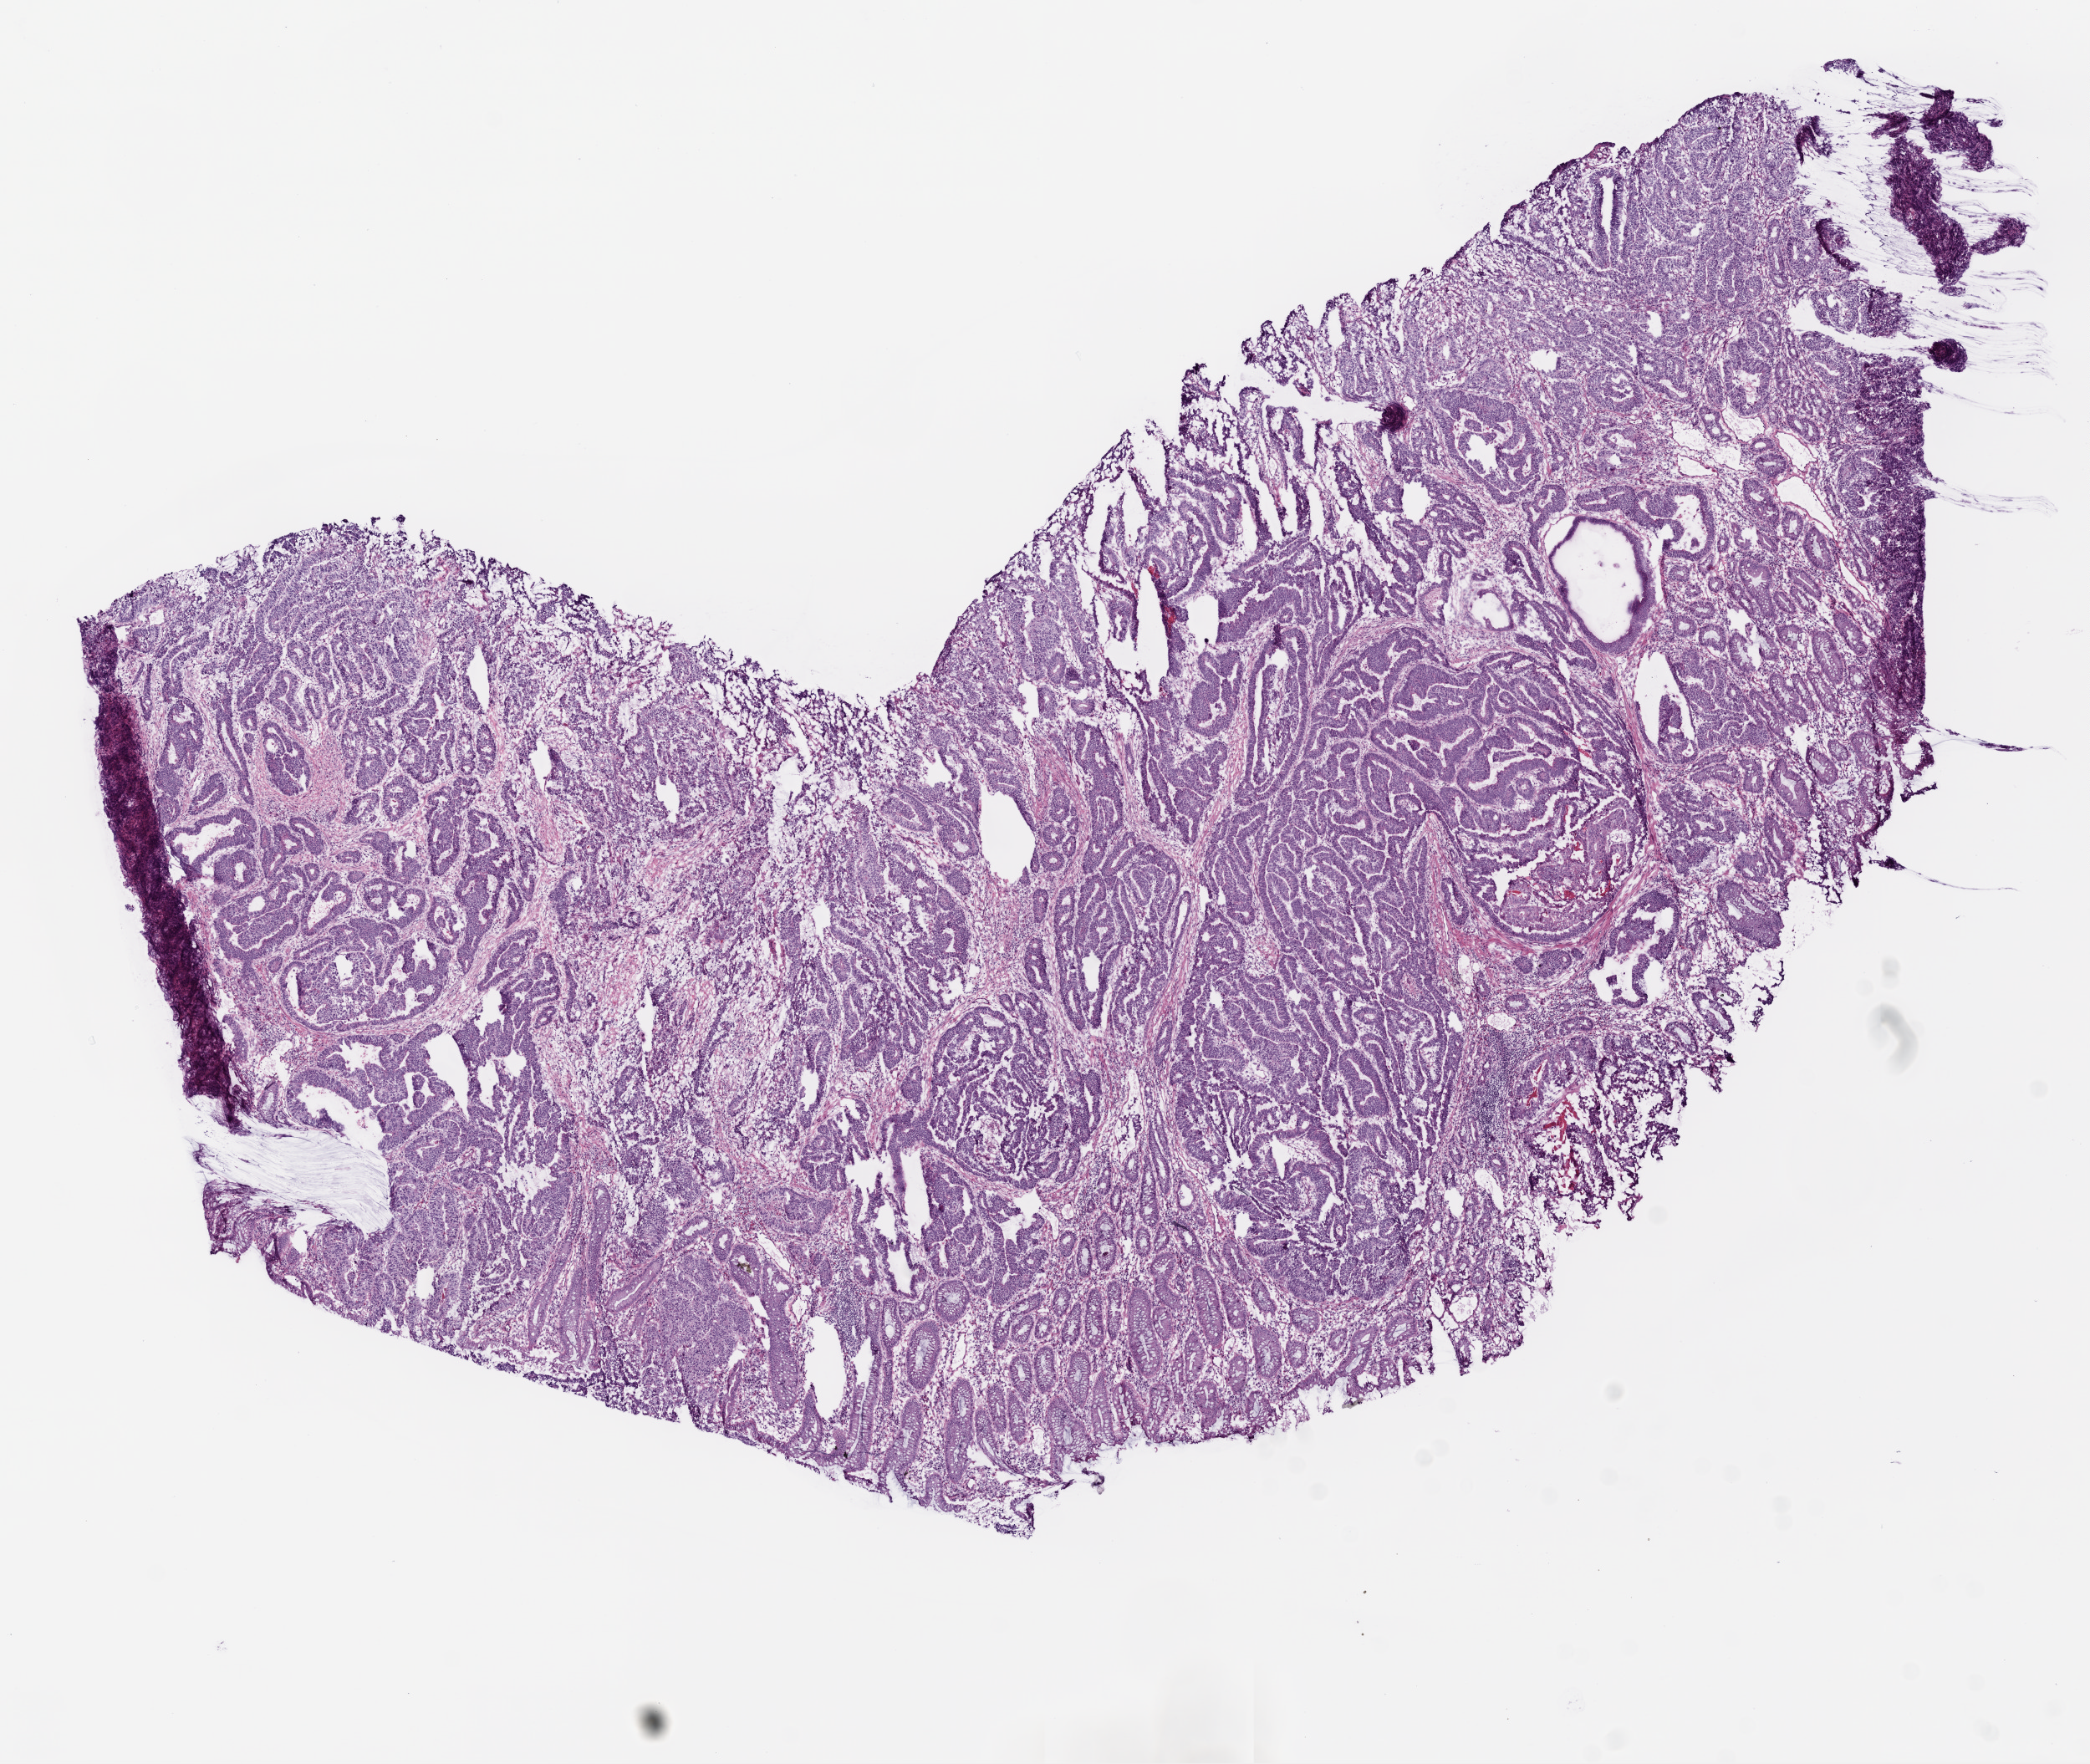
H&E-stained whole-slide image, a low-resolution overview of the entire scanned area, about 10.0 x 8.5 mm (from a 20x scan). Frozen section. Sample: primary tumour, colon. Male, age 80 years at initial diagnosis. Pathologist review of this section (percent, as recorded): tumour cells 90%, tumour nuclei 95%, normal cells 0%, stromal cells 10%, necrosis 0%.
• AJCC pathologic stage: I (6th edition)
• diagnosis: Adenocarcinoma, NOS